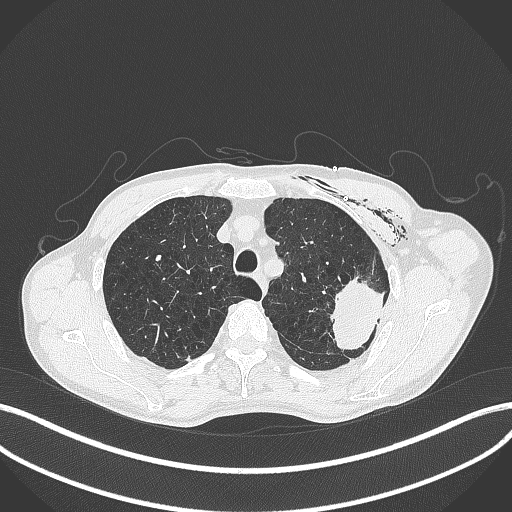
Chest CT, one axial slice; position 326 of 457 along the scan axis; 120 kVp; lung window (W 1500 / L -600 HU); 1 mm slice thickness; 512 × 512 image matrix, field of view 400 × 400 mm. Patient: male, 58 years. From the clinical record (not read from this slice): clinical TNM (as recorded): T3 N0 M0.
Outlined on this slice (bounding box drawn by a radiologist):
- lung tumour (recorded histology: adenocarcinoma): bounding box [x1, y1, x2, y2] px = [329, 276, 387, 357]